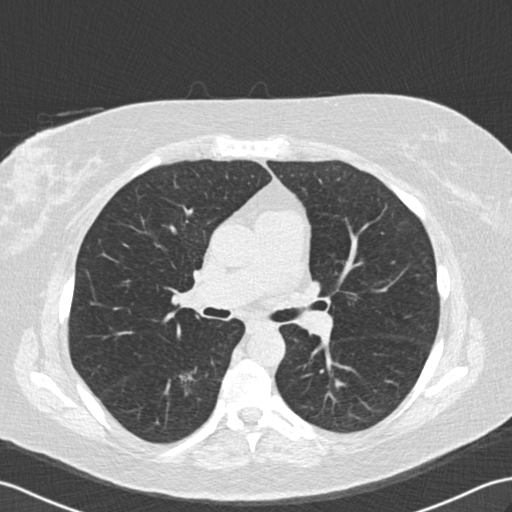
Low-dose screening chest CT, one axial slice; reconstruction kernel B30f; lung window (W 1500 / L -600 HU); 512 × 512 image matrix, field of view 352 × 352 mm.
Structures marked on this image (outlined manually by an expert reader):
- lesion 1 (tumor, lower lobe of right lung): bounding box [x1, y1, x2, y2] px = [179, 372, 195, 396]